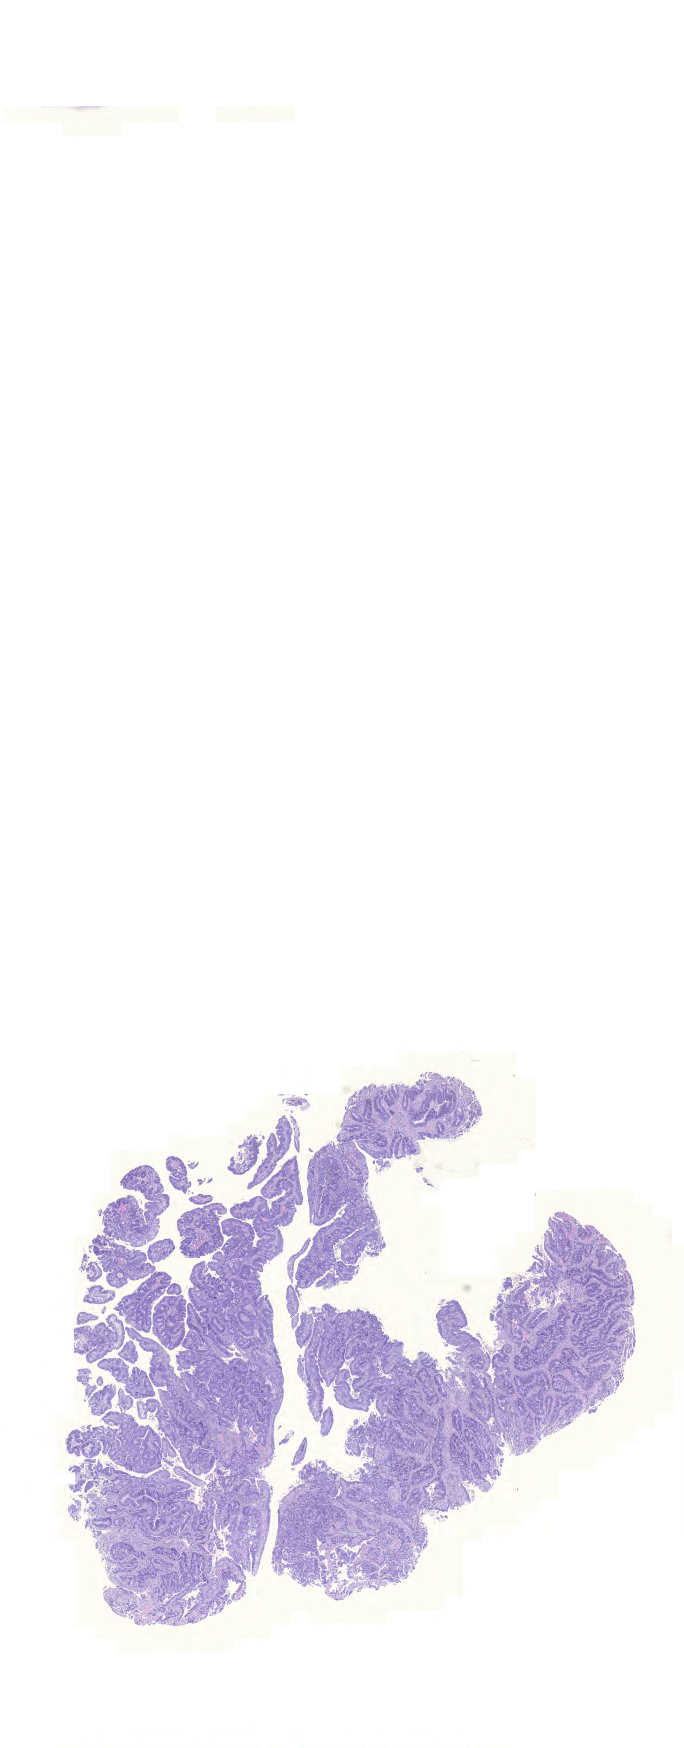
Whole-slide histology image, Hematoxylin and eosin (H&E) stained, low-resolution overview of the scanned area, about 10.2 x 26.0 mm (acquisition: 20x scan); formalin-fixed paraffin-embedded (FFPE) diagnostic section; colon, primary tumour sample. Female patient.
Pathologic diagnosis: Adenocarcinoma, NOS. Lymph nodes positive (case pathology): 0 of 19 examined. AJCC pathologic stage: I (6th edition).